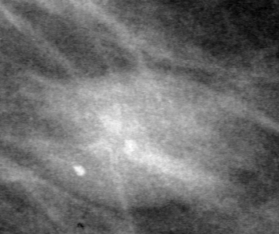
Crop from a digitized film mammogram around one marked abnormality, right breast, MLO view, BI-RADS breast density category 2 (scale 1–4).
Finding: mass, shape oval, margins circumscribed; BI-RADS assessment category 3; pathology result (as recorded, not read from the image): benign.